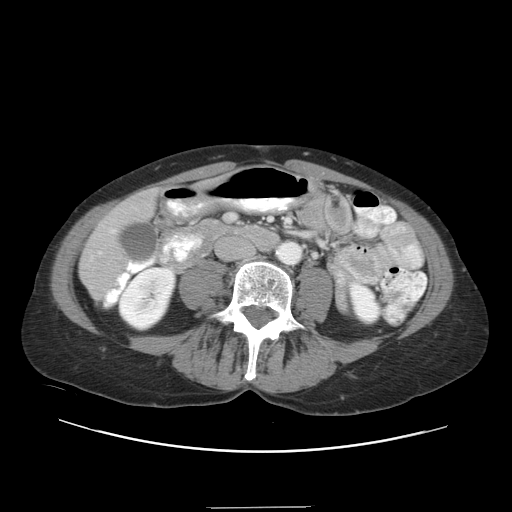
Contrast-enhanced abdominal CT, one axial slice; reconstruction kernel STANDARD; intravenous contrast given; soft-tissue window (W 400 / L 40 HU); 5 mm slice thickness; 512 × 512 image matrix, field of view 388 × 388 mm. Female patient, age 64 years. Case-level facts recorded for this patient, not image findings: diagnosis: colorectal cancer liver metastases, imaged before liver resection; multiple liver metastases: no; largest metastasis: 3.8 cm; chemotherapy before resection: yes.
Annotated regions visible in this slice (manually delineated by an expert):
- hepatic veins: box from (x=110, y=229) to (x=115, y=233) px
- liver: (x=81, y=192)–(x=156, y=294)